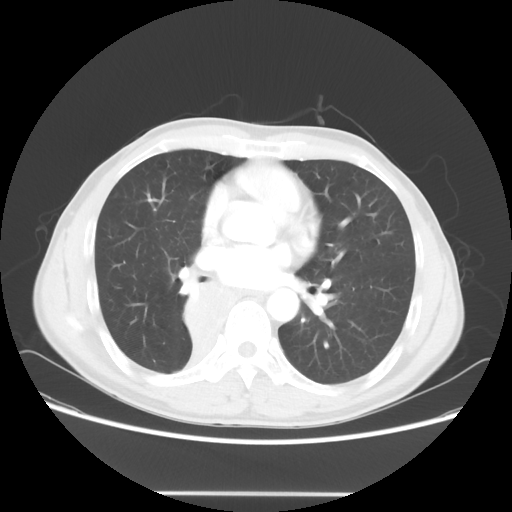
Chest CT, one axial slice; slice 31 of 62 in the series (ordered by position); reconstruction kernel STANDARD; 120 kVp; lung window (W 1500 / L -600 HU); 5 mm slice thickness; 512 × 512 image matrix, field of view 393 × 393 mm. Male patient, age 47 years. Case-level facts recorded for this patient, not image findings: clinical TNM (as recorded): T2 N0 M0; histopathological grade: G2.
Structures marked on this image (bounding box drawn by a radiologist):
- lung tumour (recorded histology: squamous cell carcinoma): box from (x=170, y=271) to (x=235, y=365) px